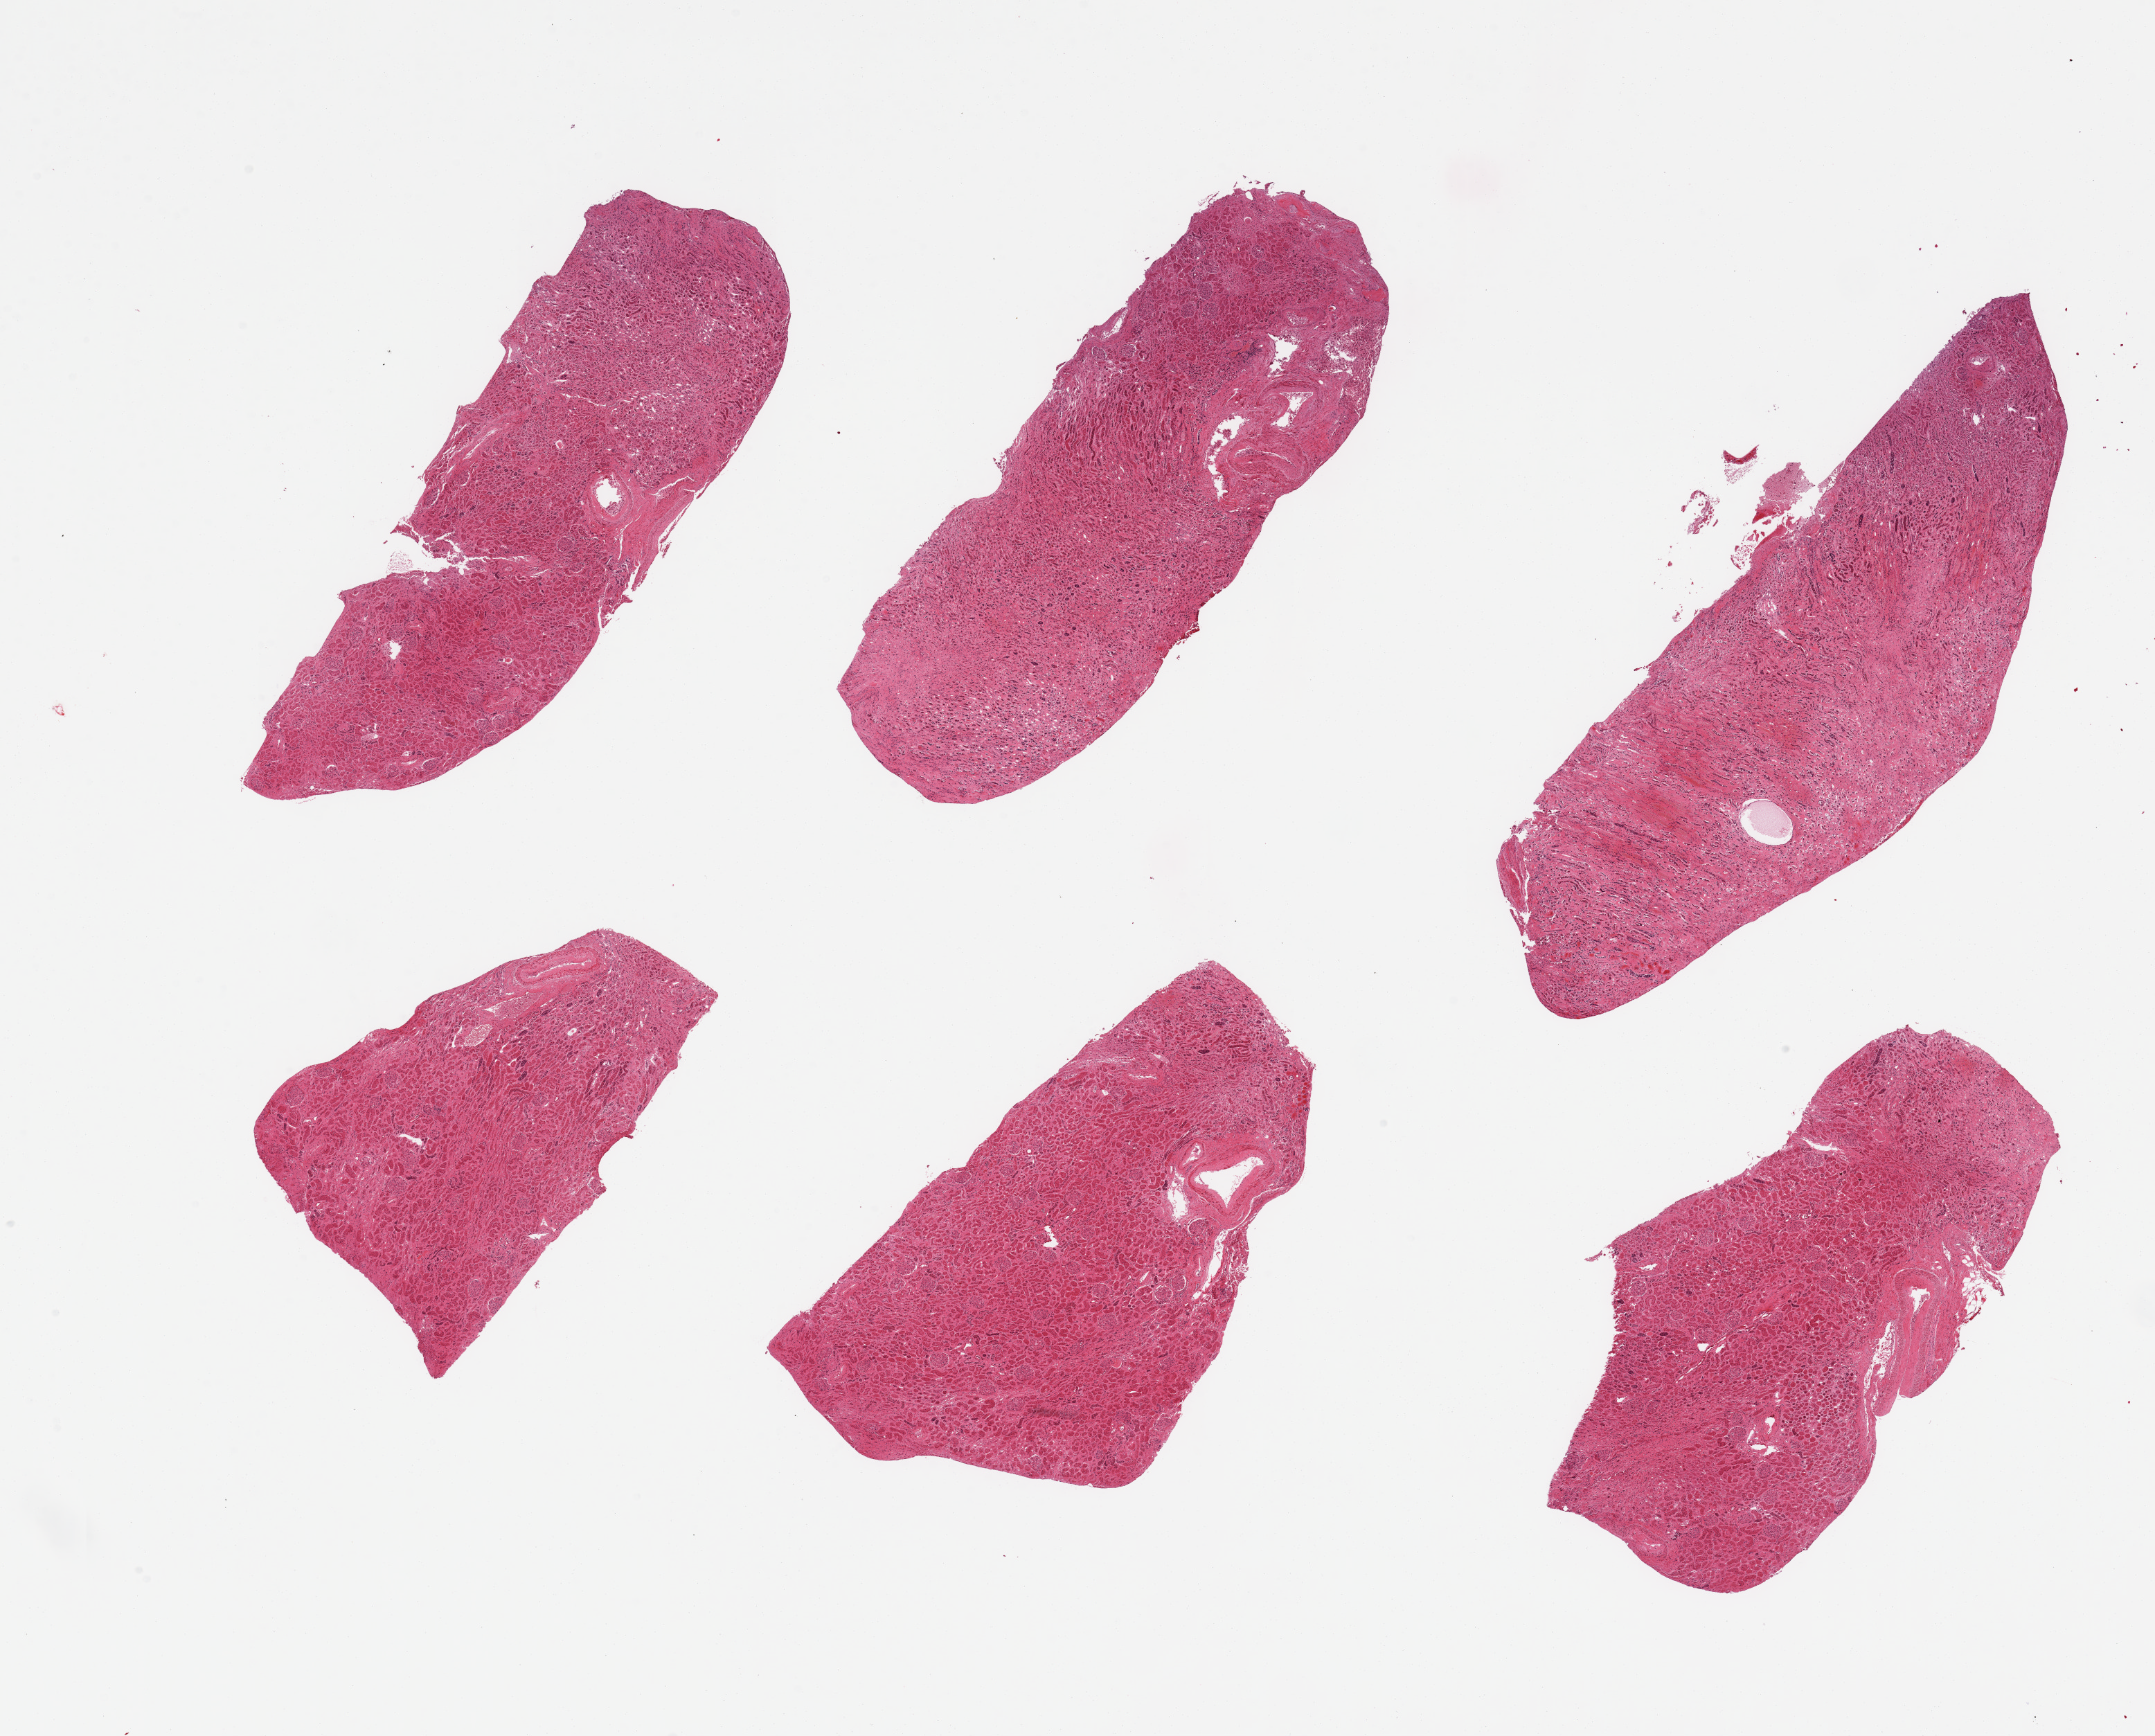
Whole-slide image, H&E stain, brightfield, low-resolution overview of the scanned area, about 24.6 x 19.8 mm, PAXgene-fixed paraffin-embedded (PFPE) section, sampled site (target tissue): renal cortex, donor tissue sample.
Pathologist's review note for this sample: 6 pieces: over 50% is medulla.